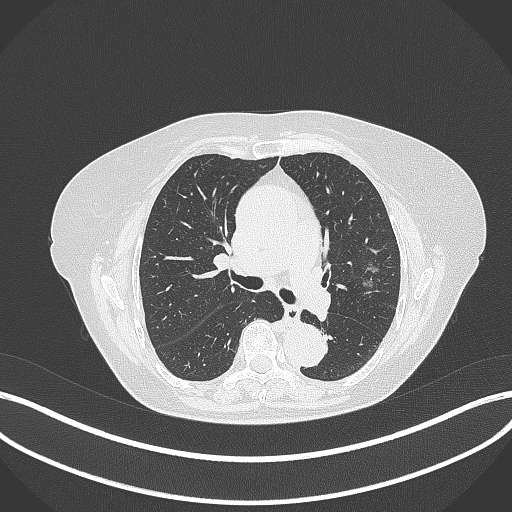
Chest CT, one axial slice; slice 201 of 316 in the series (ordered by position); reconstruction kernel B70f; 120 kVp; lung window (W 1500 / L -600 HU); 1 mm slice thickness; 512 × 512 image matrix, field of view 400 × 400 mm. Female patient, age 75 years. From the clinical record (not read from this slice): clinical TNM (as recorded): T1c N0 M0.
Outlined on this slice (bounding box drawn by a radiologist):
- lung tumour (recorded histology: adenocarcinoma): bounding box <361,259,380,292> (left, top, right, bottom; pixels)